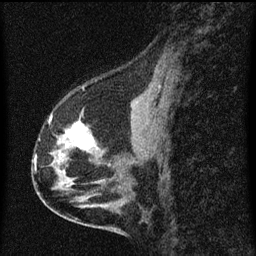
Breast MRI (dynamic contrast-enhanced), one sagittal slice; position 30 of 60 along the scan axis; dynamic contrast-enhanced series, image 2 of 3 at this slice position (ordered by acquisition); 1.5 T; TE 4.2 ms, TR 8 ms; 2 mm slice thickness; 256 × 256 image matrix, field of view 180 × 180 mm. Patient: female, 56 years.
Structures marked on this image (semi-automatic segmentation, software-assisted and operator-edited):
- analysis volume of interest (the breast-tissue region the enhancement analysis was run in; not a lesion): box from (x=48, y=115) to (x=102, y=181) px
- tumour enhancement mask (voxels above the 70 % enhancement threshold inside the analysis volume of interest): (x=67, y=121)–(x=93, y=150)